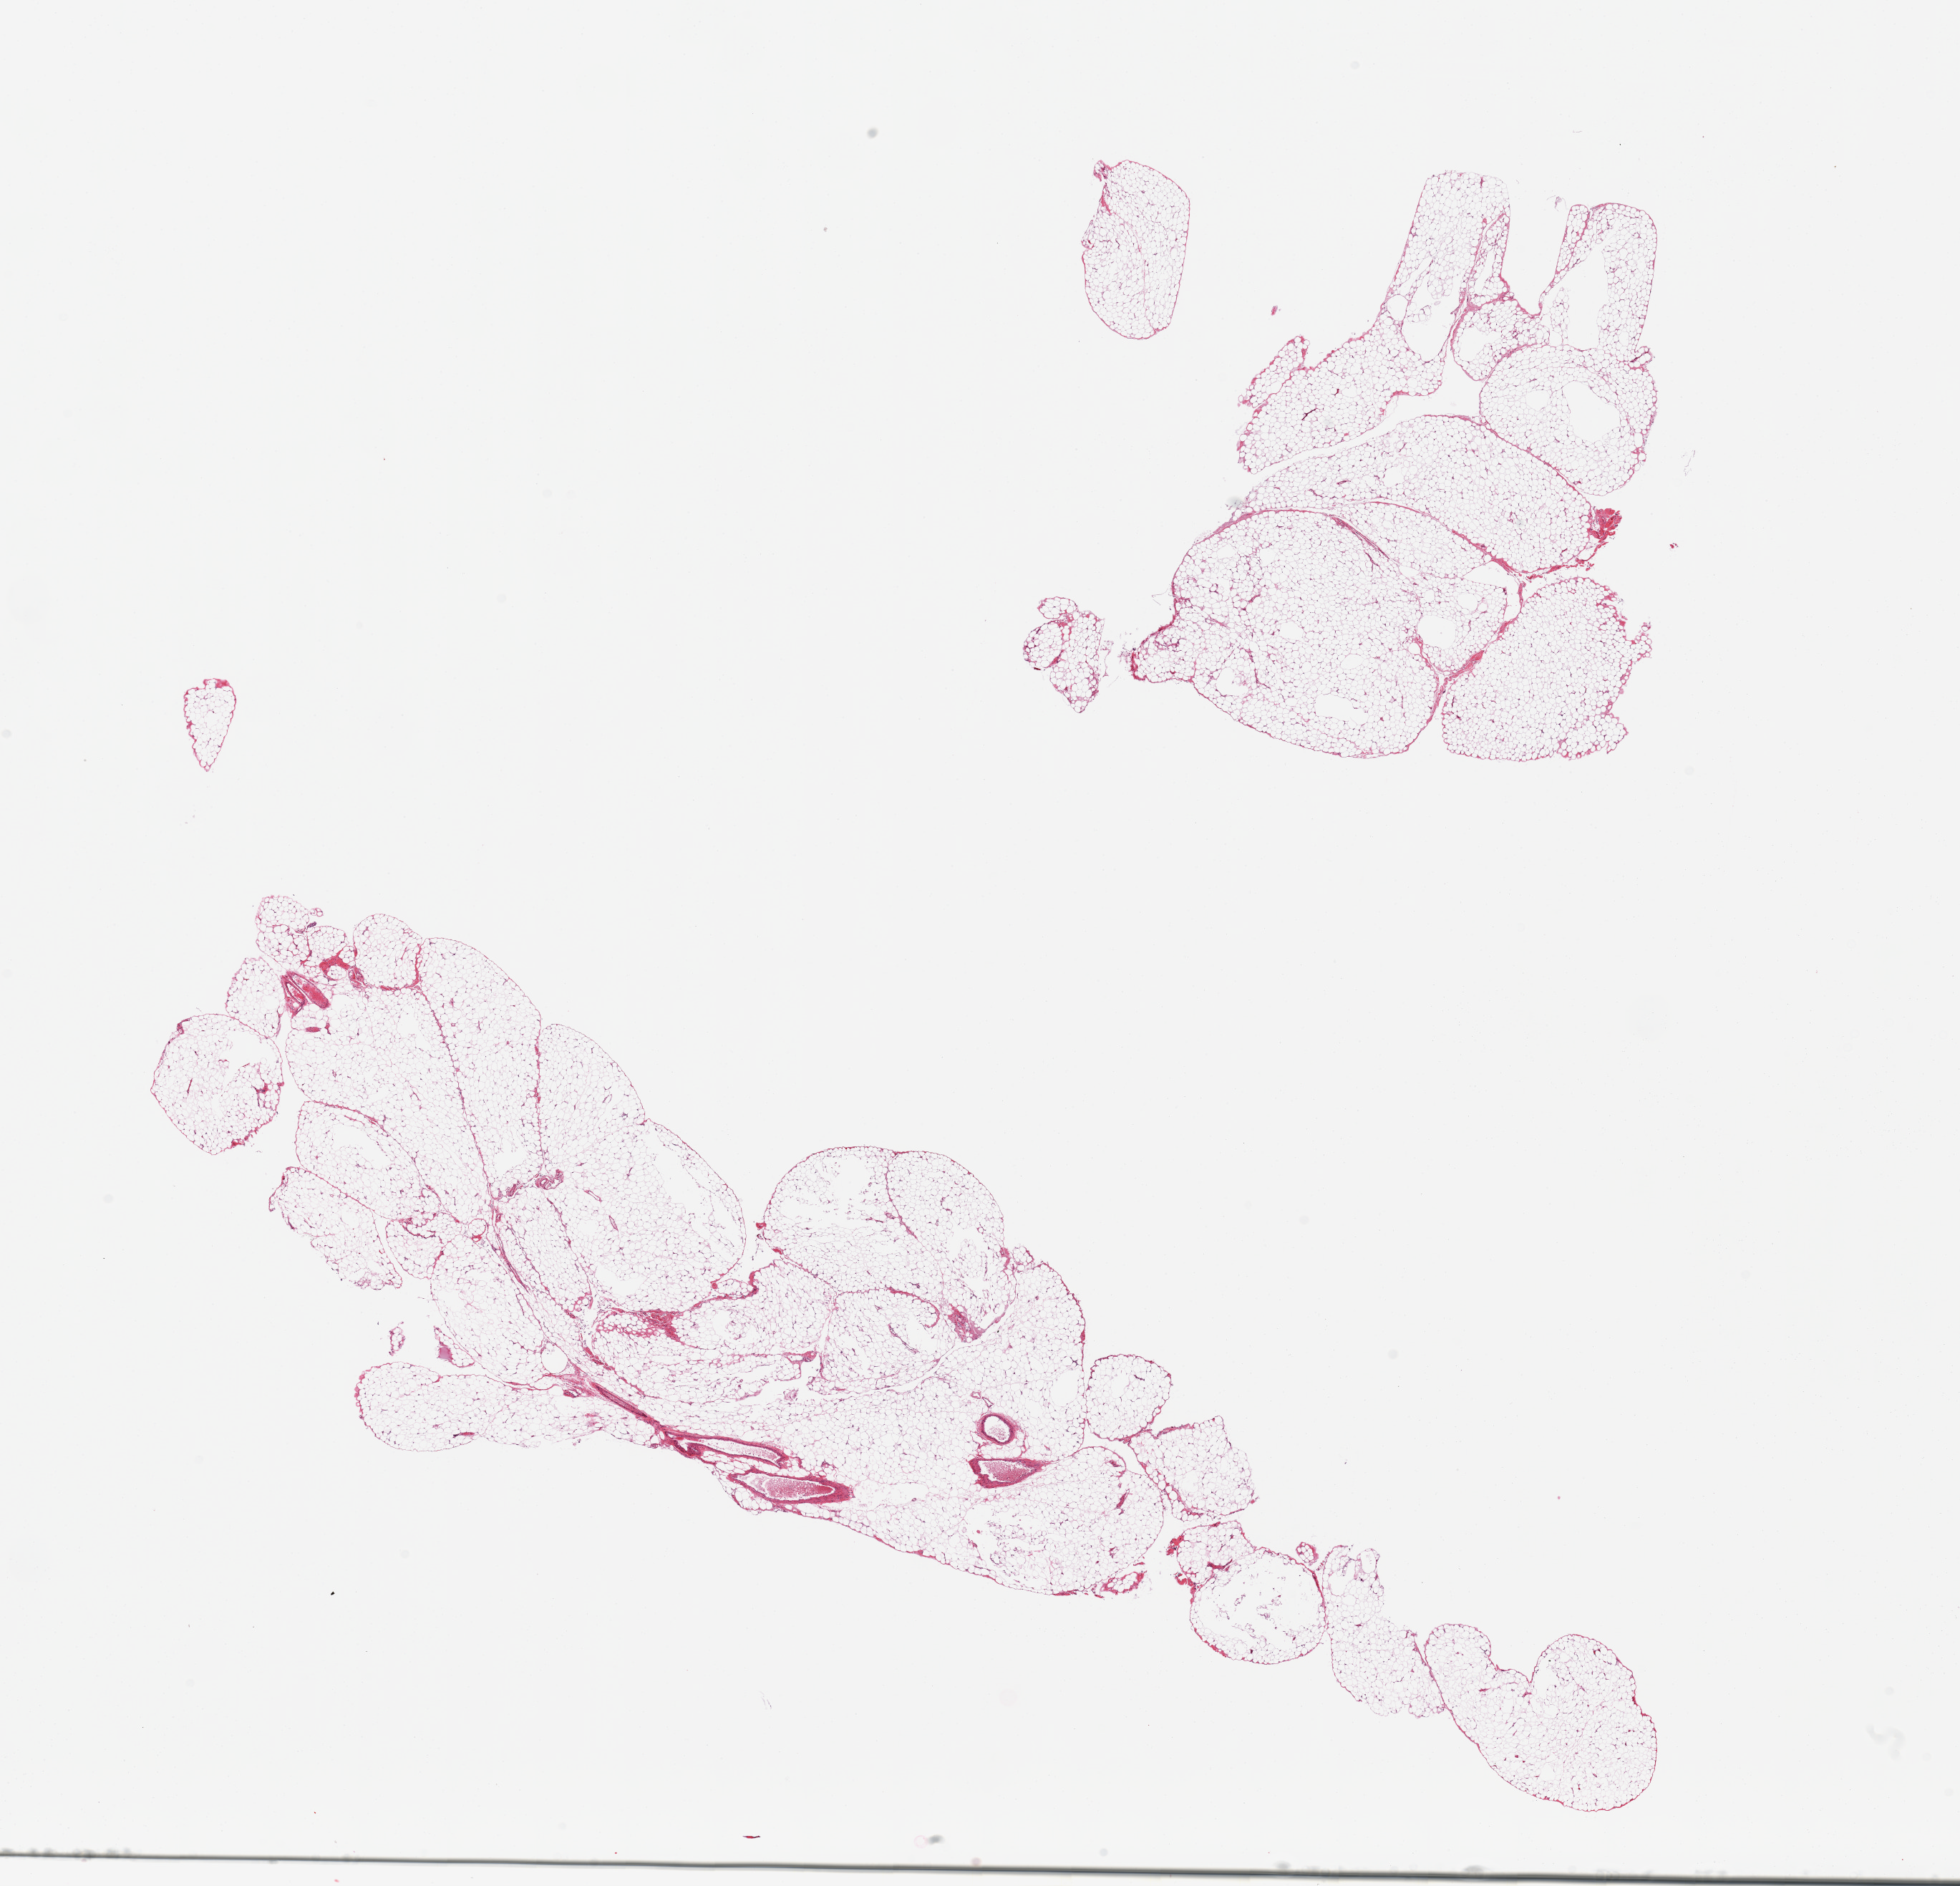
Haematoxylin and eosin whole-slide image, whole scanned area (about 21.7 x 20.8 mm) shown as a low-resolution overview; PAXgene-fixed paraffin-embedded (PFPE) section; sampled site (target tissue): omentum; tissue donor sample. Donor: female.
Review note (as recorded): 2 pieces, minimal fibrous/vascular tissue.